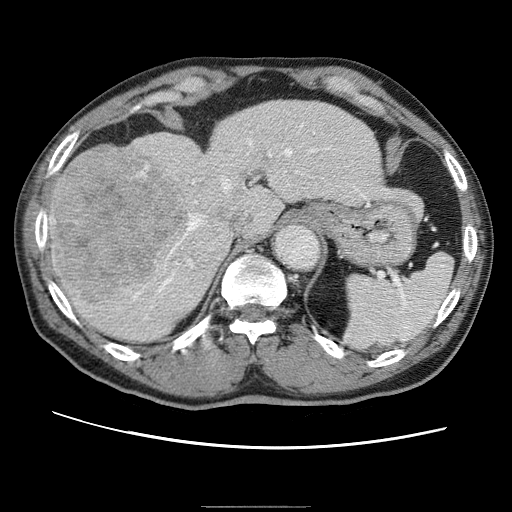
Contrast-enhanced abdominal CT (liver protocol), one axial slice. Slice 43 of 75 in the series (ordered by position). Reconstruction kernel STANDARD. One of 2 acquisitions stored at this slice position. Soft-tissue window (W 400 / L 40 HU). 2.5 mm slice thickness. 512 × 512 image matrix, field of view 360 × 360 mm. Case-level facts recorded for this patient, not image findings: diagnosis: hepatocellular carcinoma (patient treated with transarterial chemoembolisation; whether this scan precedes or follows treatment is not stated here); TNM stage (as recorded): Stage-II; Child-Pugh class: A; tumour differentiation: well differentiated; tumour size: 2 cm.
Outlined on this slice (semi-automatically segmented with operator editing):
- abdominal aorta: bounding box [x1, y1, x2, y2] px = [274, 225, 318, 268]
- liver parenchyma outside the tumour (the mass and vessels are separate outlines, so this box may not span the whole liver): [50, 100, 392, 342]
- mass: [49, 149, 182, 297]
- liver vessels: [163, 130, 366, 286]